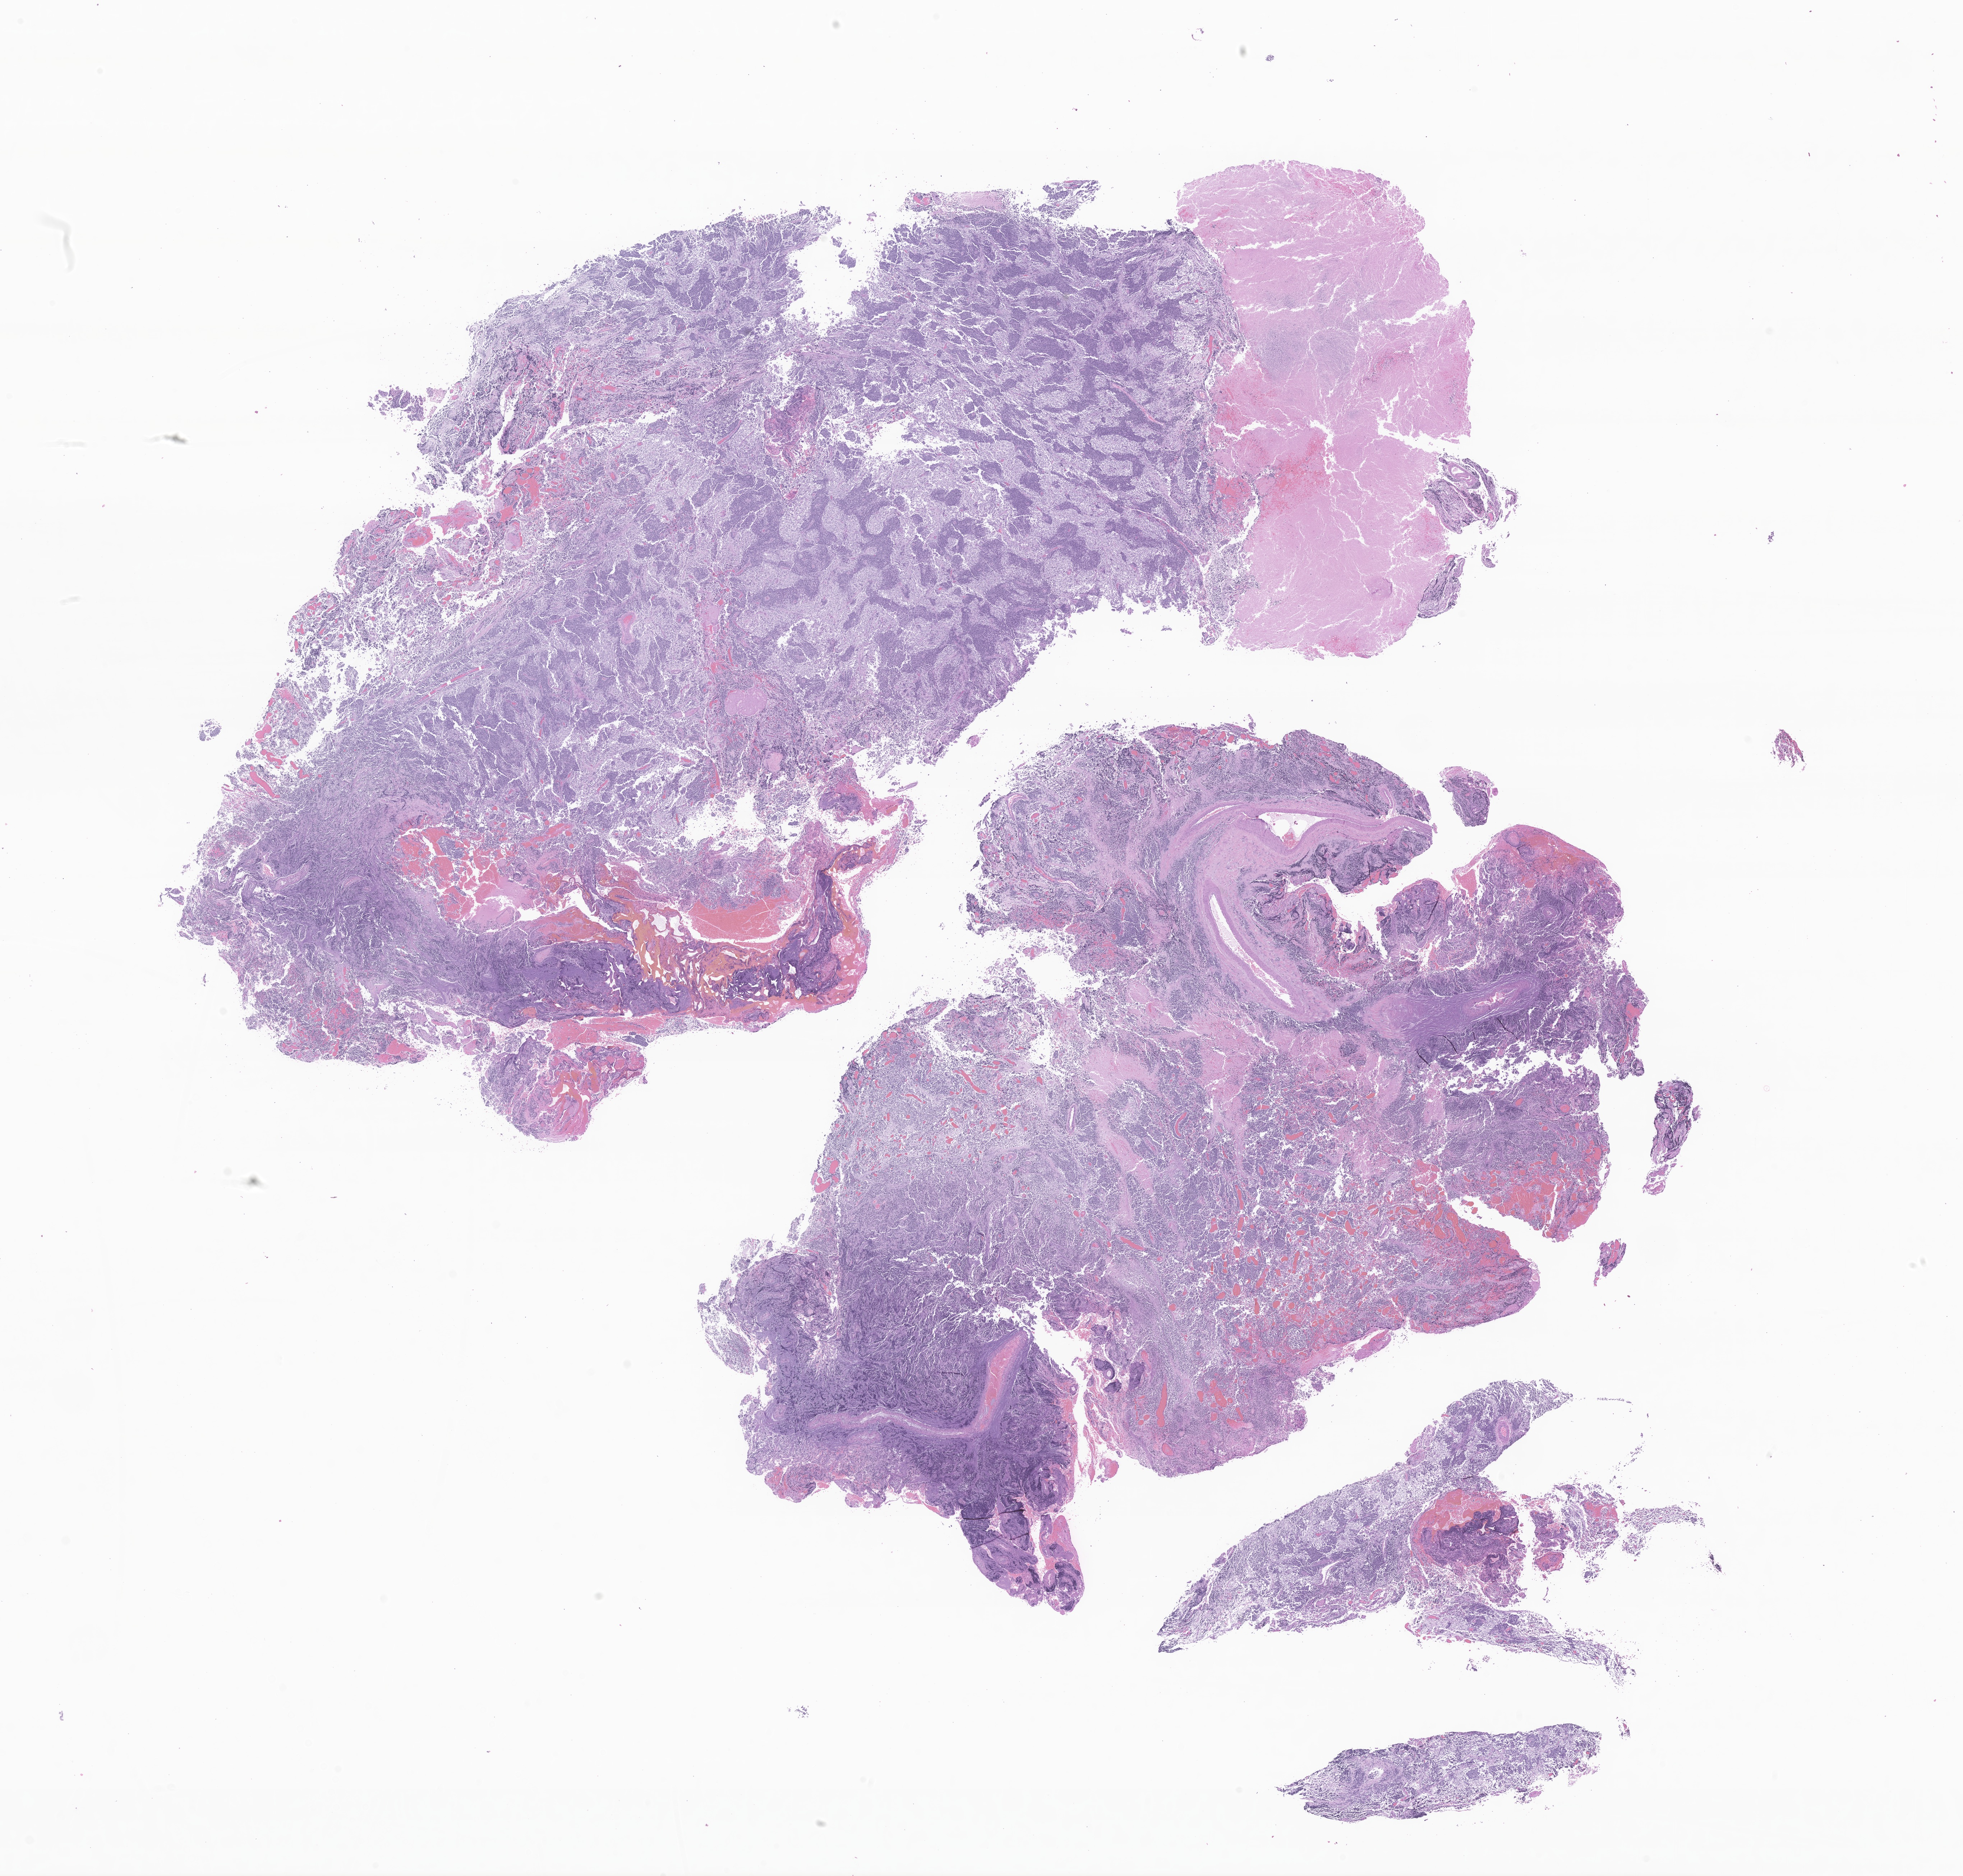
Digitized H&E-stained section of tumor tissue from the brain, low-resolution overview of the scanned area, about 23.0 x 22.0 mm, FFPE section. Patient: male, age 96 months (8 years).
Recorded diagnosis: Medulloblastoma, NOS.